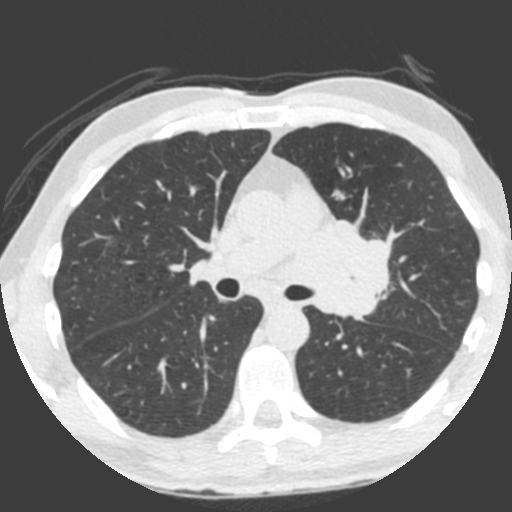
Low-dose screening chest CT, one axial slice; lung window (W 1500 / L -600 HU); 512 × 512 image matrix, field of view 315 × 315 mm.
Annotated regions visible in this slice (expert manual segmentation):
- lesion 1 (tumor, upper lobe of left lung): bounding box <315,220,392,320> (left, top, right, bottom; pixels)